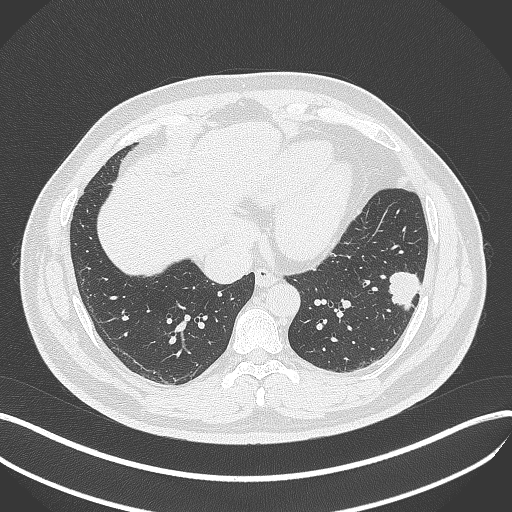
Chest CT, one axial slice; slice 136 of 429 in the series (ordered by position); reconstruction kernel B70f; 120 kVp; lung window (W 1500 / L -600 HU); 1 mm slice thickness; 512 × 512 image matrix. Male patient, age 39 years. From the clinical record (not read from this slice): clinical TNM (as recorded): T2a N0 M0; histopathological grade: G2-3.
Structures marked on this image (bounding box drawn by a radiologist):
- lung tumour (recorded histology: adenocarcinoma): bounding box [x1, y1, x2, y2] px = [387, 267, 425, 310]